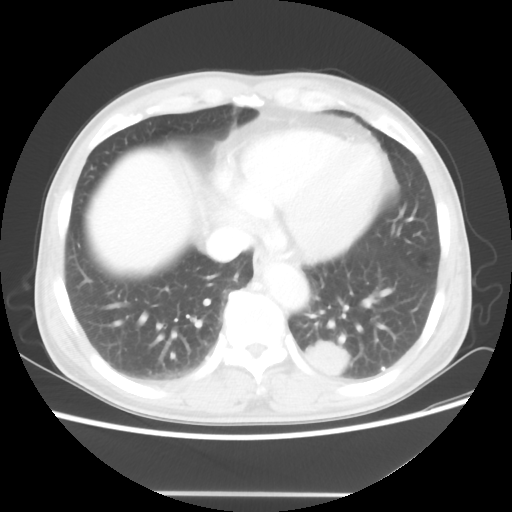
Chest CT, one axial slice. Position 18 of 60 along the scan axis. 100 kVp. Lung window (W 1500 / L -600 HU). 5 mm slice thickness. 512 × 512 image matrix. Male patient, age 55 years. From the clinical record (not read from this slice): clinical TNM (as recorded): T1c N3 M0.
Annotated regions visible in this slice (bounding box drawn by a radiologist):
- lung tumour (recorded histology: small cell carcinoma): bounding box (x1, y1, x2, y2) in pixels: (295, 334, 348, 384)